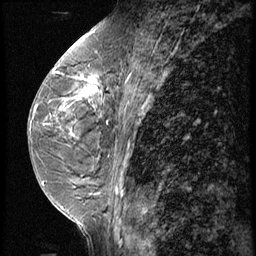
Breast MRI (dynamic contrast-enhanced), one sagittal slice. 3 images stored at this slice position (order not interpretable as contrast timing). 1.5 T. TE 4.2 ms, TR 9 ms. 2.5 mm slice thickness. 256 × 256 image matrix, field of view 180 × 180 mm. Patient: female, 44 years. From the clinical record (not read from this slice): setting: breast cancer imaged before/during neoadjuvant chemotherapy; receptor status: triple-negative.
Structures marked on this image (semi-automatic segmentation, software-assisted and operator-edited):
- analysis volume of interest (the breast-tissue region the enhancement analysis was run in; not a lesion): bounding box (x1, y1, x2, y2) in pixels: (67, 64, 116, 125)
- tumour enhancement mask (voxels above the 140 % enhancement threshold inside the analysis volume of interest): (68, 77, 111, 124)